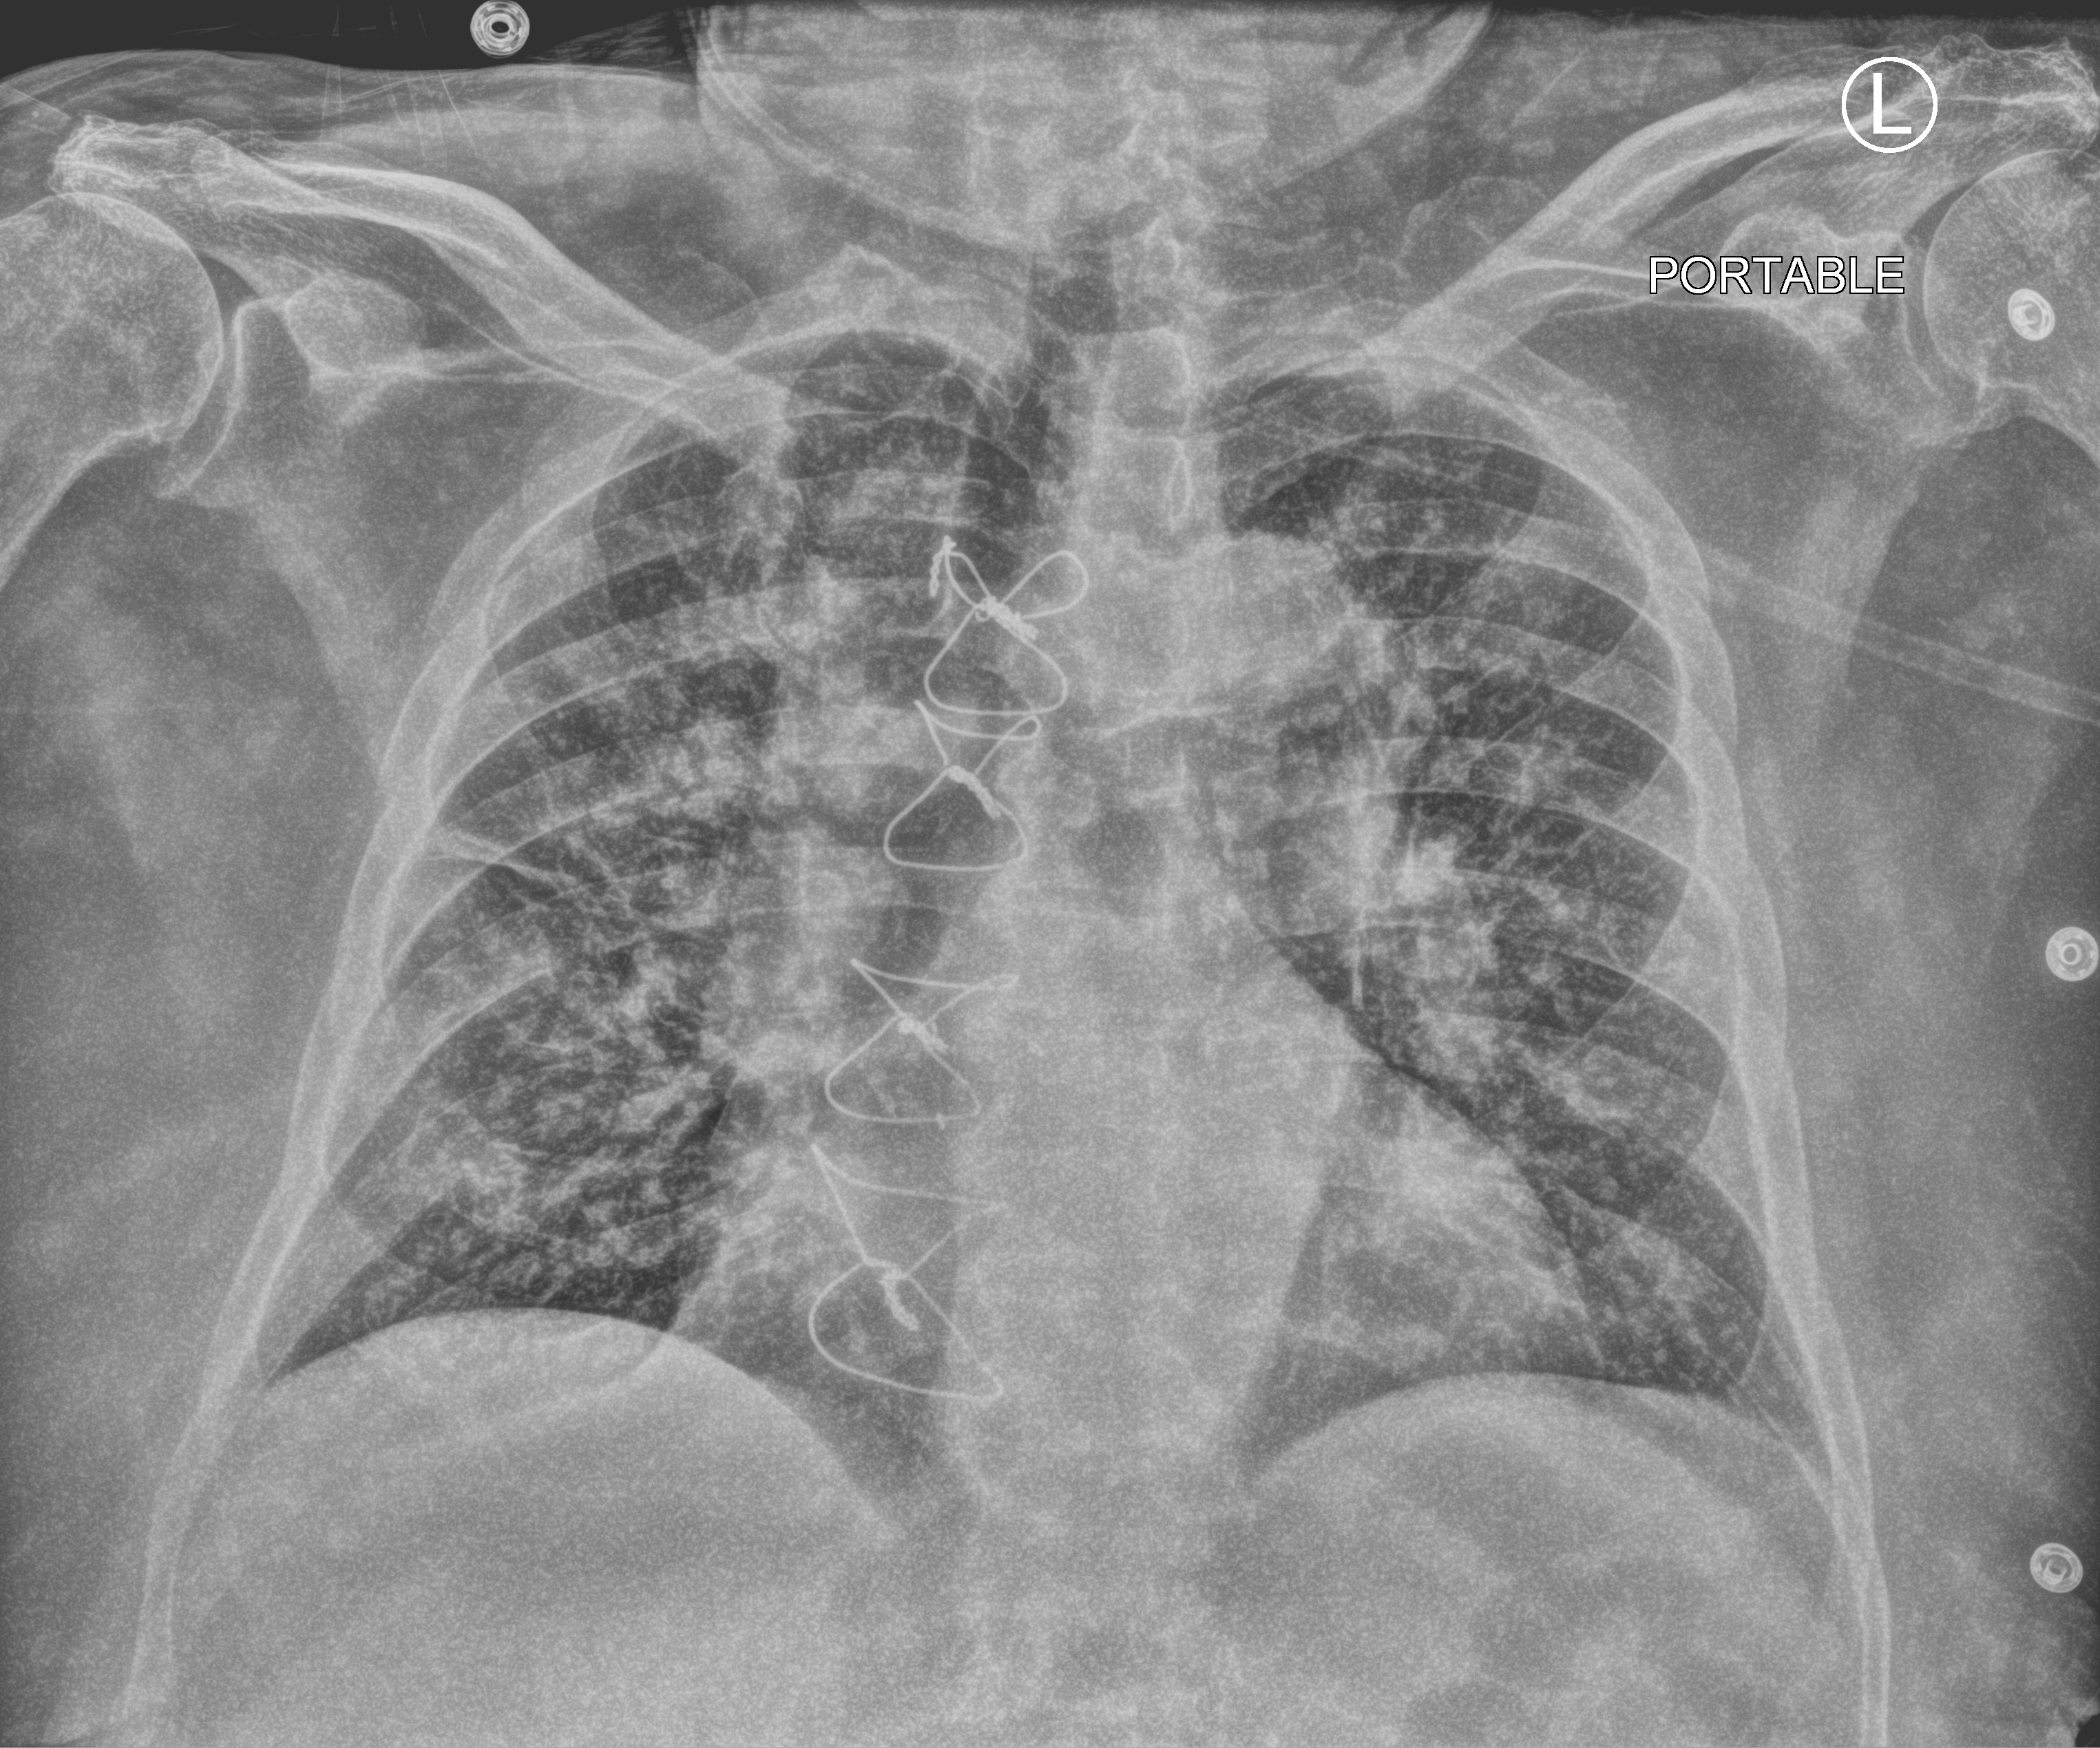
Bedside chest radiograph (computed radiography), anteroposterior (AP) projection. Male patient hospitalised with COVID-19, age 75–90 years.
Admission-level facts for this patient (not findings on this image; timing relative to this image not recorded): other chronic lung disease (admission record): no; admitted to intensive care during this hospital stay: no; mechanically ventilated during this hospital stay: no.